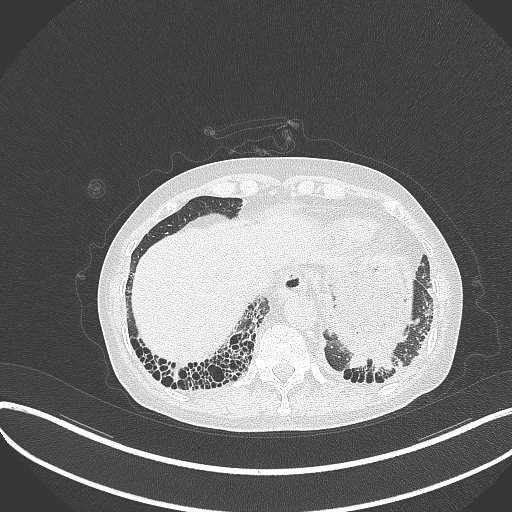
Chest CT, one axial slice. Position 54 of 373 along the scan axis. Reconstruction kernel B70f. Lung window (W 1500 / L -600 HU). 1 mm slice thickness. 512 × 512 image matrix, field of view 400 × 400 mm. Female patient, age 56 years. Case-level facts recorded for this patient, not image findings: clinical TNM (as recorded): T1 N0 M0.
Outlined on this slice (rectangle marked by the reading radiologist):
- lung tumour (recorded histology: adenocarcinoma): bounding box [x1, y1, x2, y2] px = [348, 348, 405, 378]